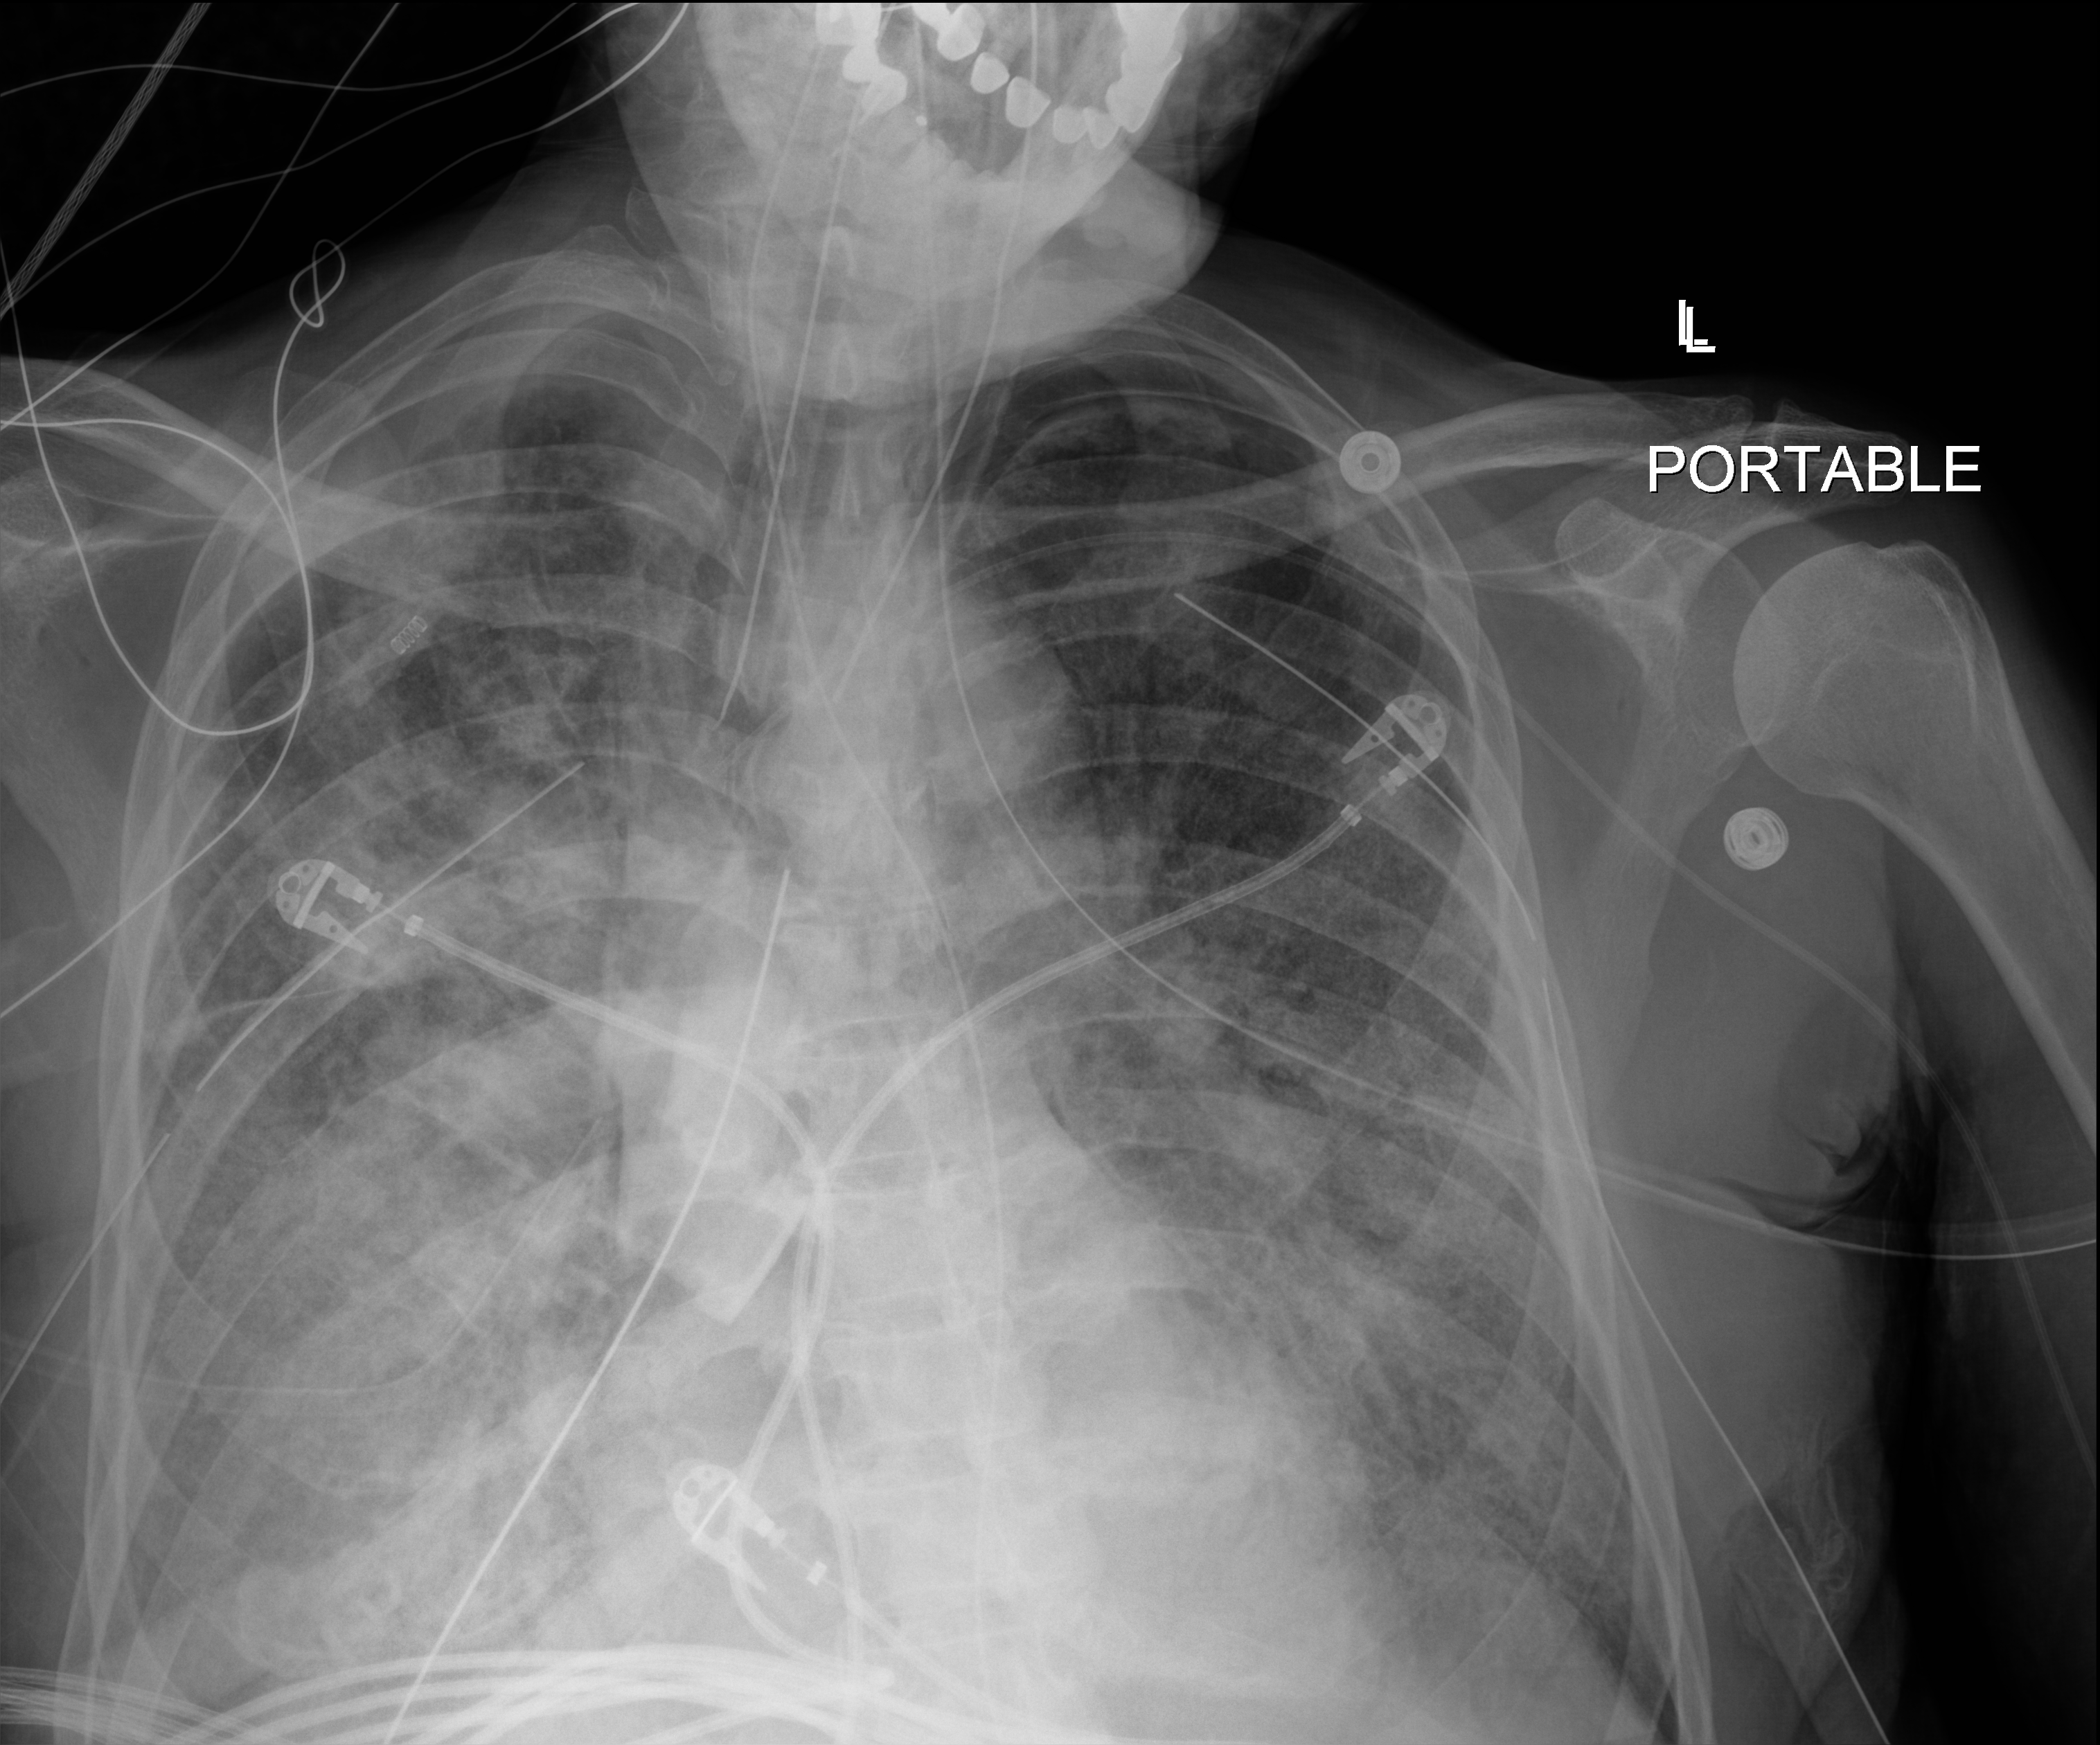
Chest X-ray (portable), anteroposterior (AP) projection. Male patient hospitalised with COVID-19, age 60–74 years.
Admission-level facts for this patient (not findings on this image; timing relative to this image not recorded): diabetes (admission record): no; hypertension (admission record): no.